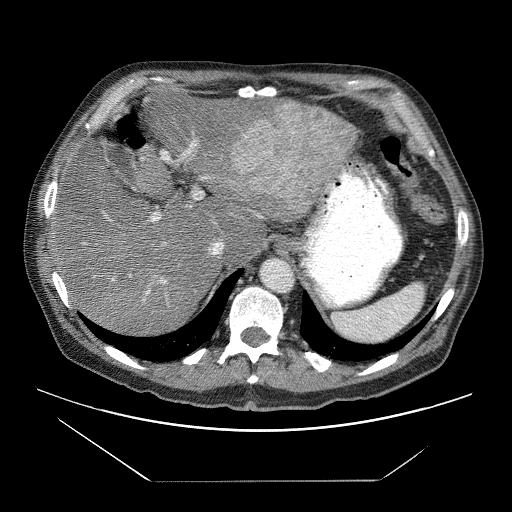
Contrast-enhanced abdominal CT (liver protocol), one axial slice. Position 51 of 83 along the scan axis. Reconstruction kernel STANDARD. 120 kVp. Soft-tissue window (W 400 / L 40 HU). 512 × 512 image matrix, field of view 420 × 420 mm. From the clinical record (not read from this slice): diagnosis: hepatocellular carcinoma (patient treated with transarterial chemoembolisation; whether this scan precedes or follows treatment is not stated here); TNM stage (as recorded): Stage-IVB; Child-Pugh class: B.
Annotated regions visible in this slice (semi-automatic segmentation, software-assisted and operator-edited):
- liver parenchyma outside the tumour (the mass and vessels are separate outlines, so this box may not span the whole liver): bounding box [x1, y1, x2, y2] px = [54, 83, 356, 334]
- mass: [233, 101, 354, 218]
- liver vessels: [82, 139, 263, 302]